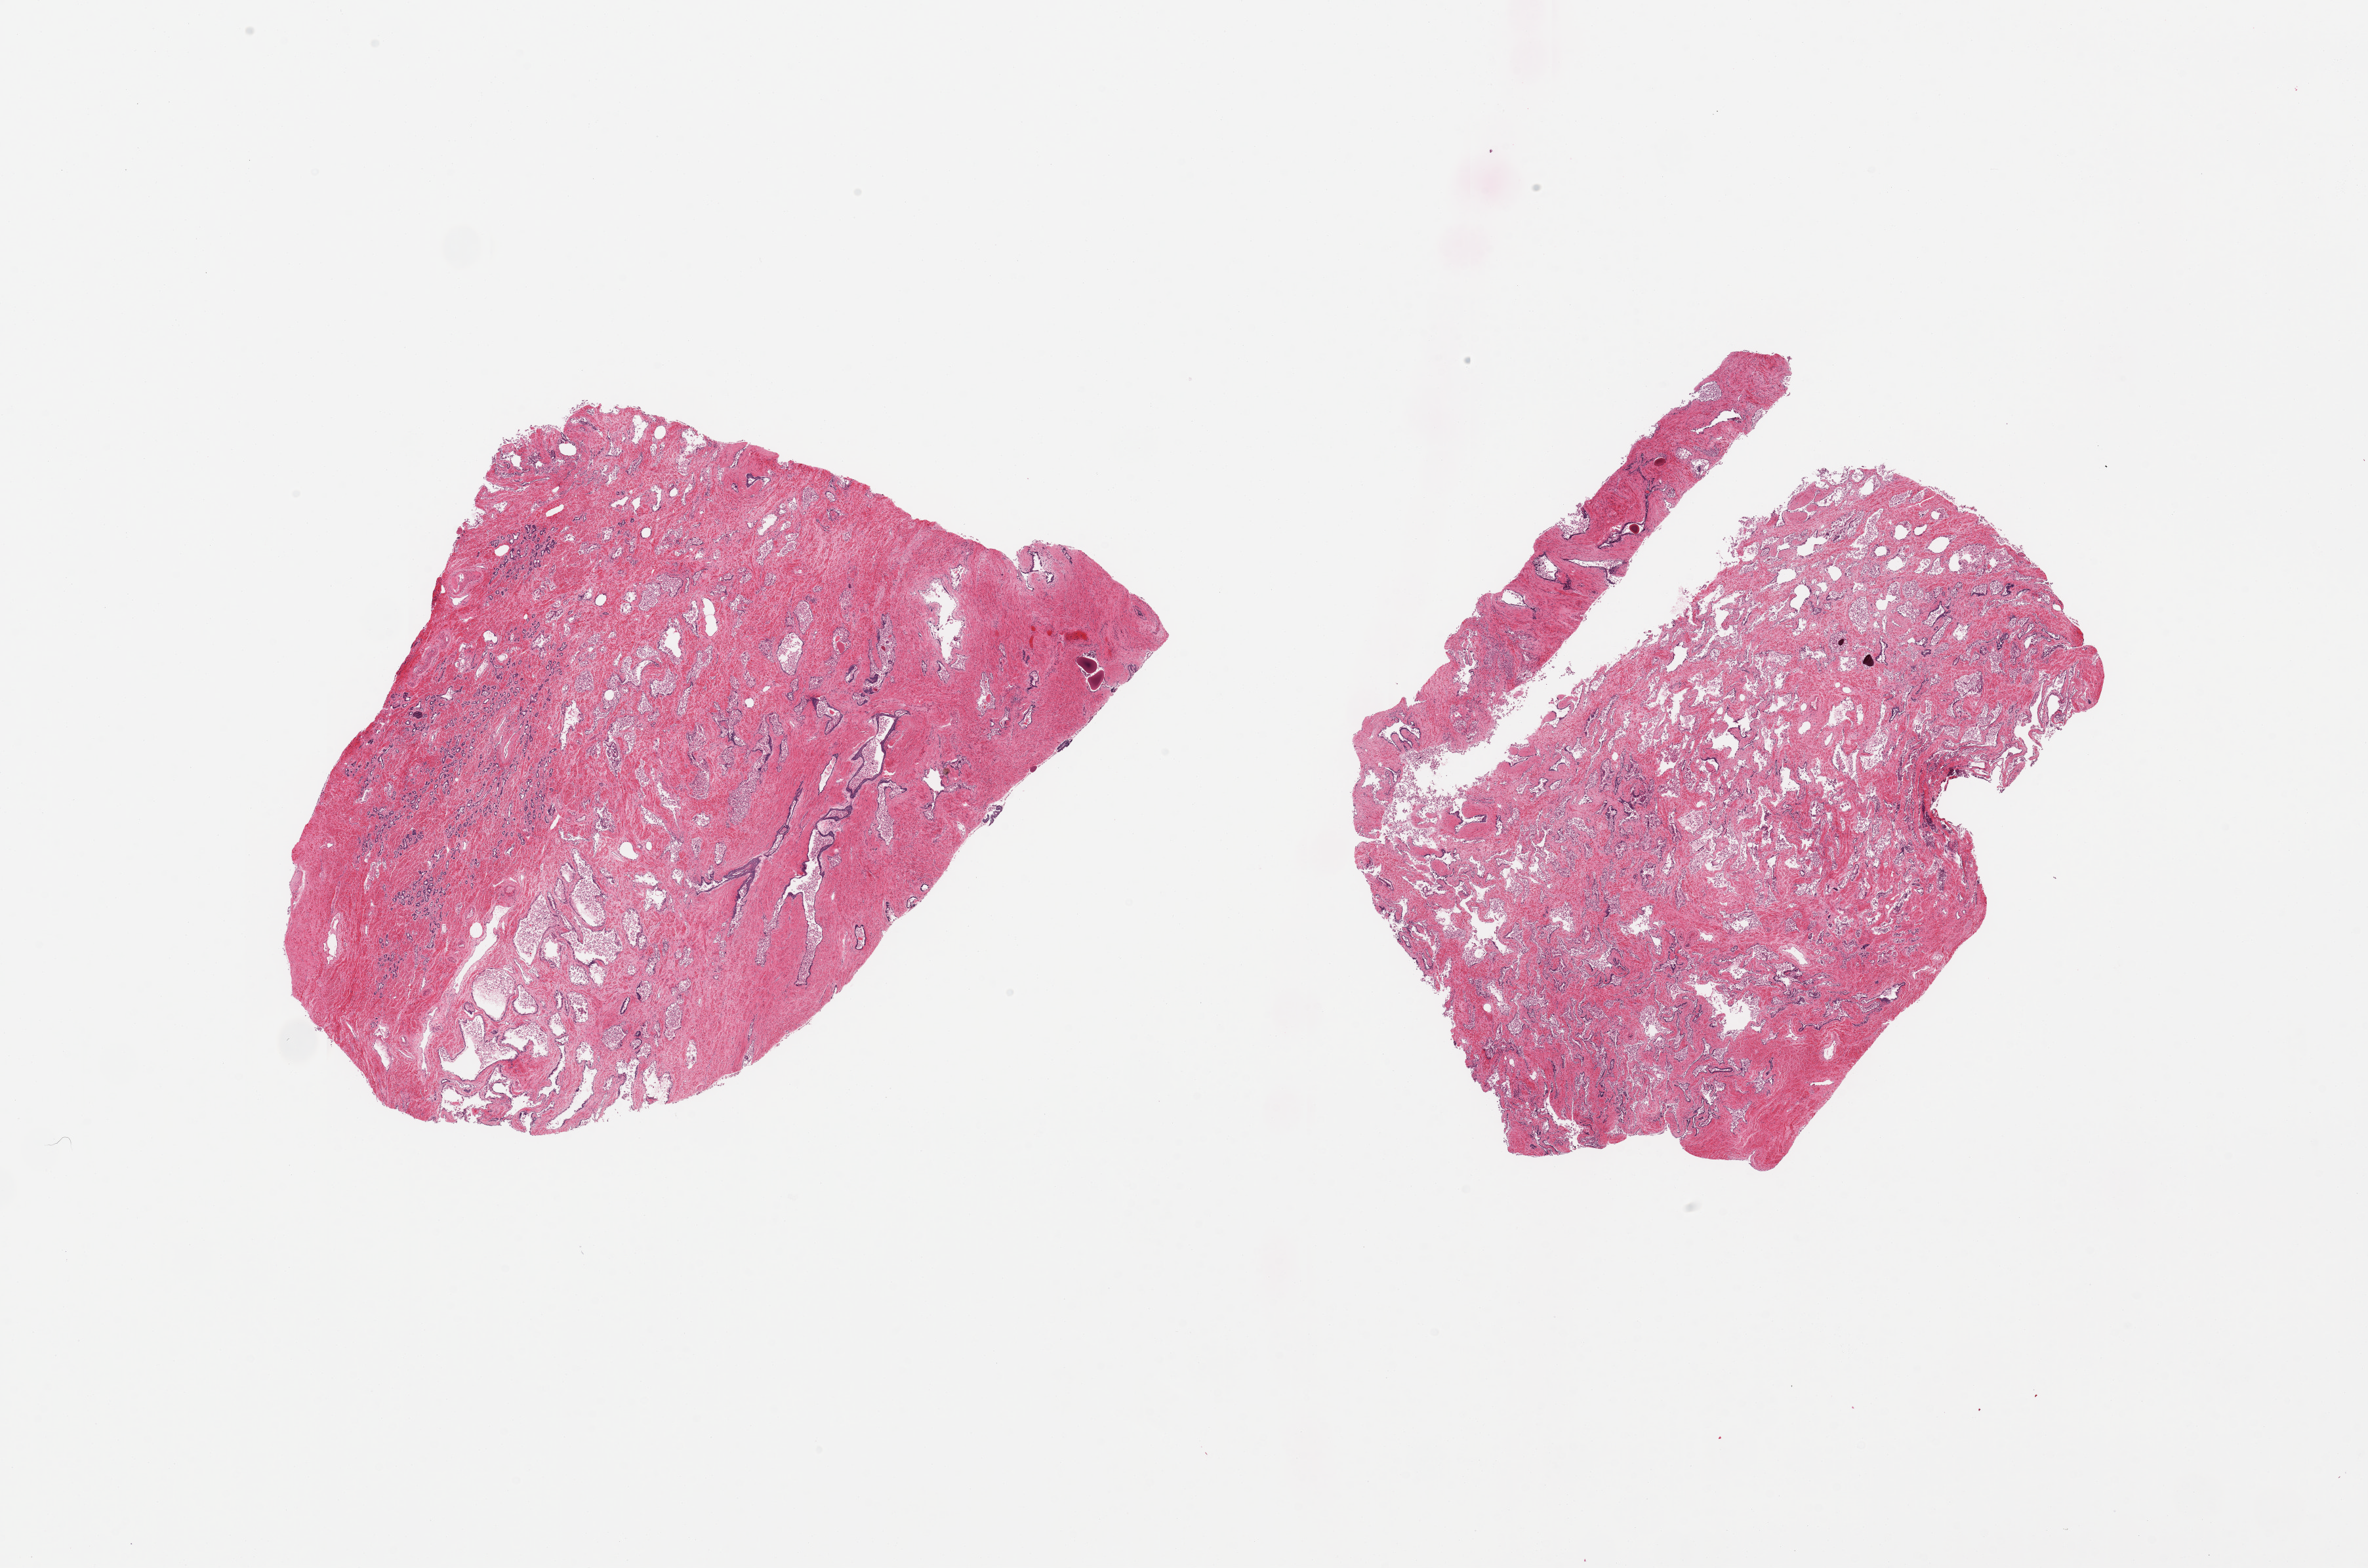
H&E whole-slide image, brightfield — a low-resolution overview of the entire scanned area, about 28.5 x 18.9 mm (acquisition: 20x scan). Donor sex: male.
• specimen: PAXgene-fixed, paraffin-embedded tissue; section of prostate (target tissue); tissue donor sample